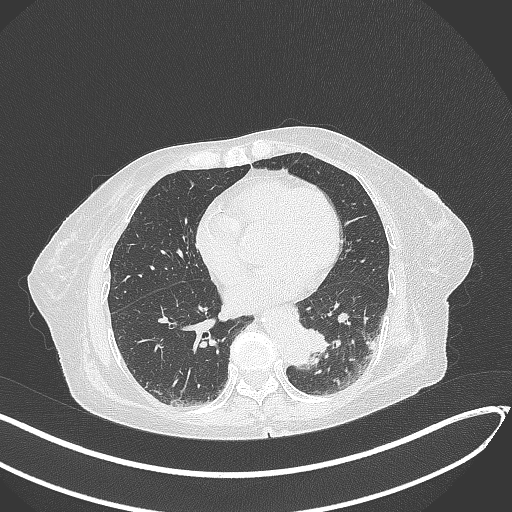
Chest CT, one axial slice. Position 88 of 324 along the scan axis. Reconstruction kernel B70f. 120 kVp. Lung window (W 1500 / L -600 HU). 1 mm slice thickness. 512 × 512 image matrix, field of view 400 × 400 mm. Patient: female, 82 years. Case-level facts recorded for this patient, not image findings: clinical TNM (as recorded): T1b N0 M1.
Annotated regions visible in this slice (bounding box drawn by a radiologist):
- lung tumour (recorded histology: adenocarcinoma): bounding box [x1, y1, x2, y2] px = [302, 325, 333, 361]